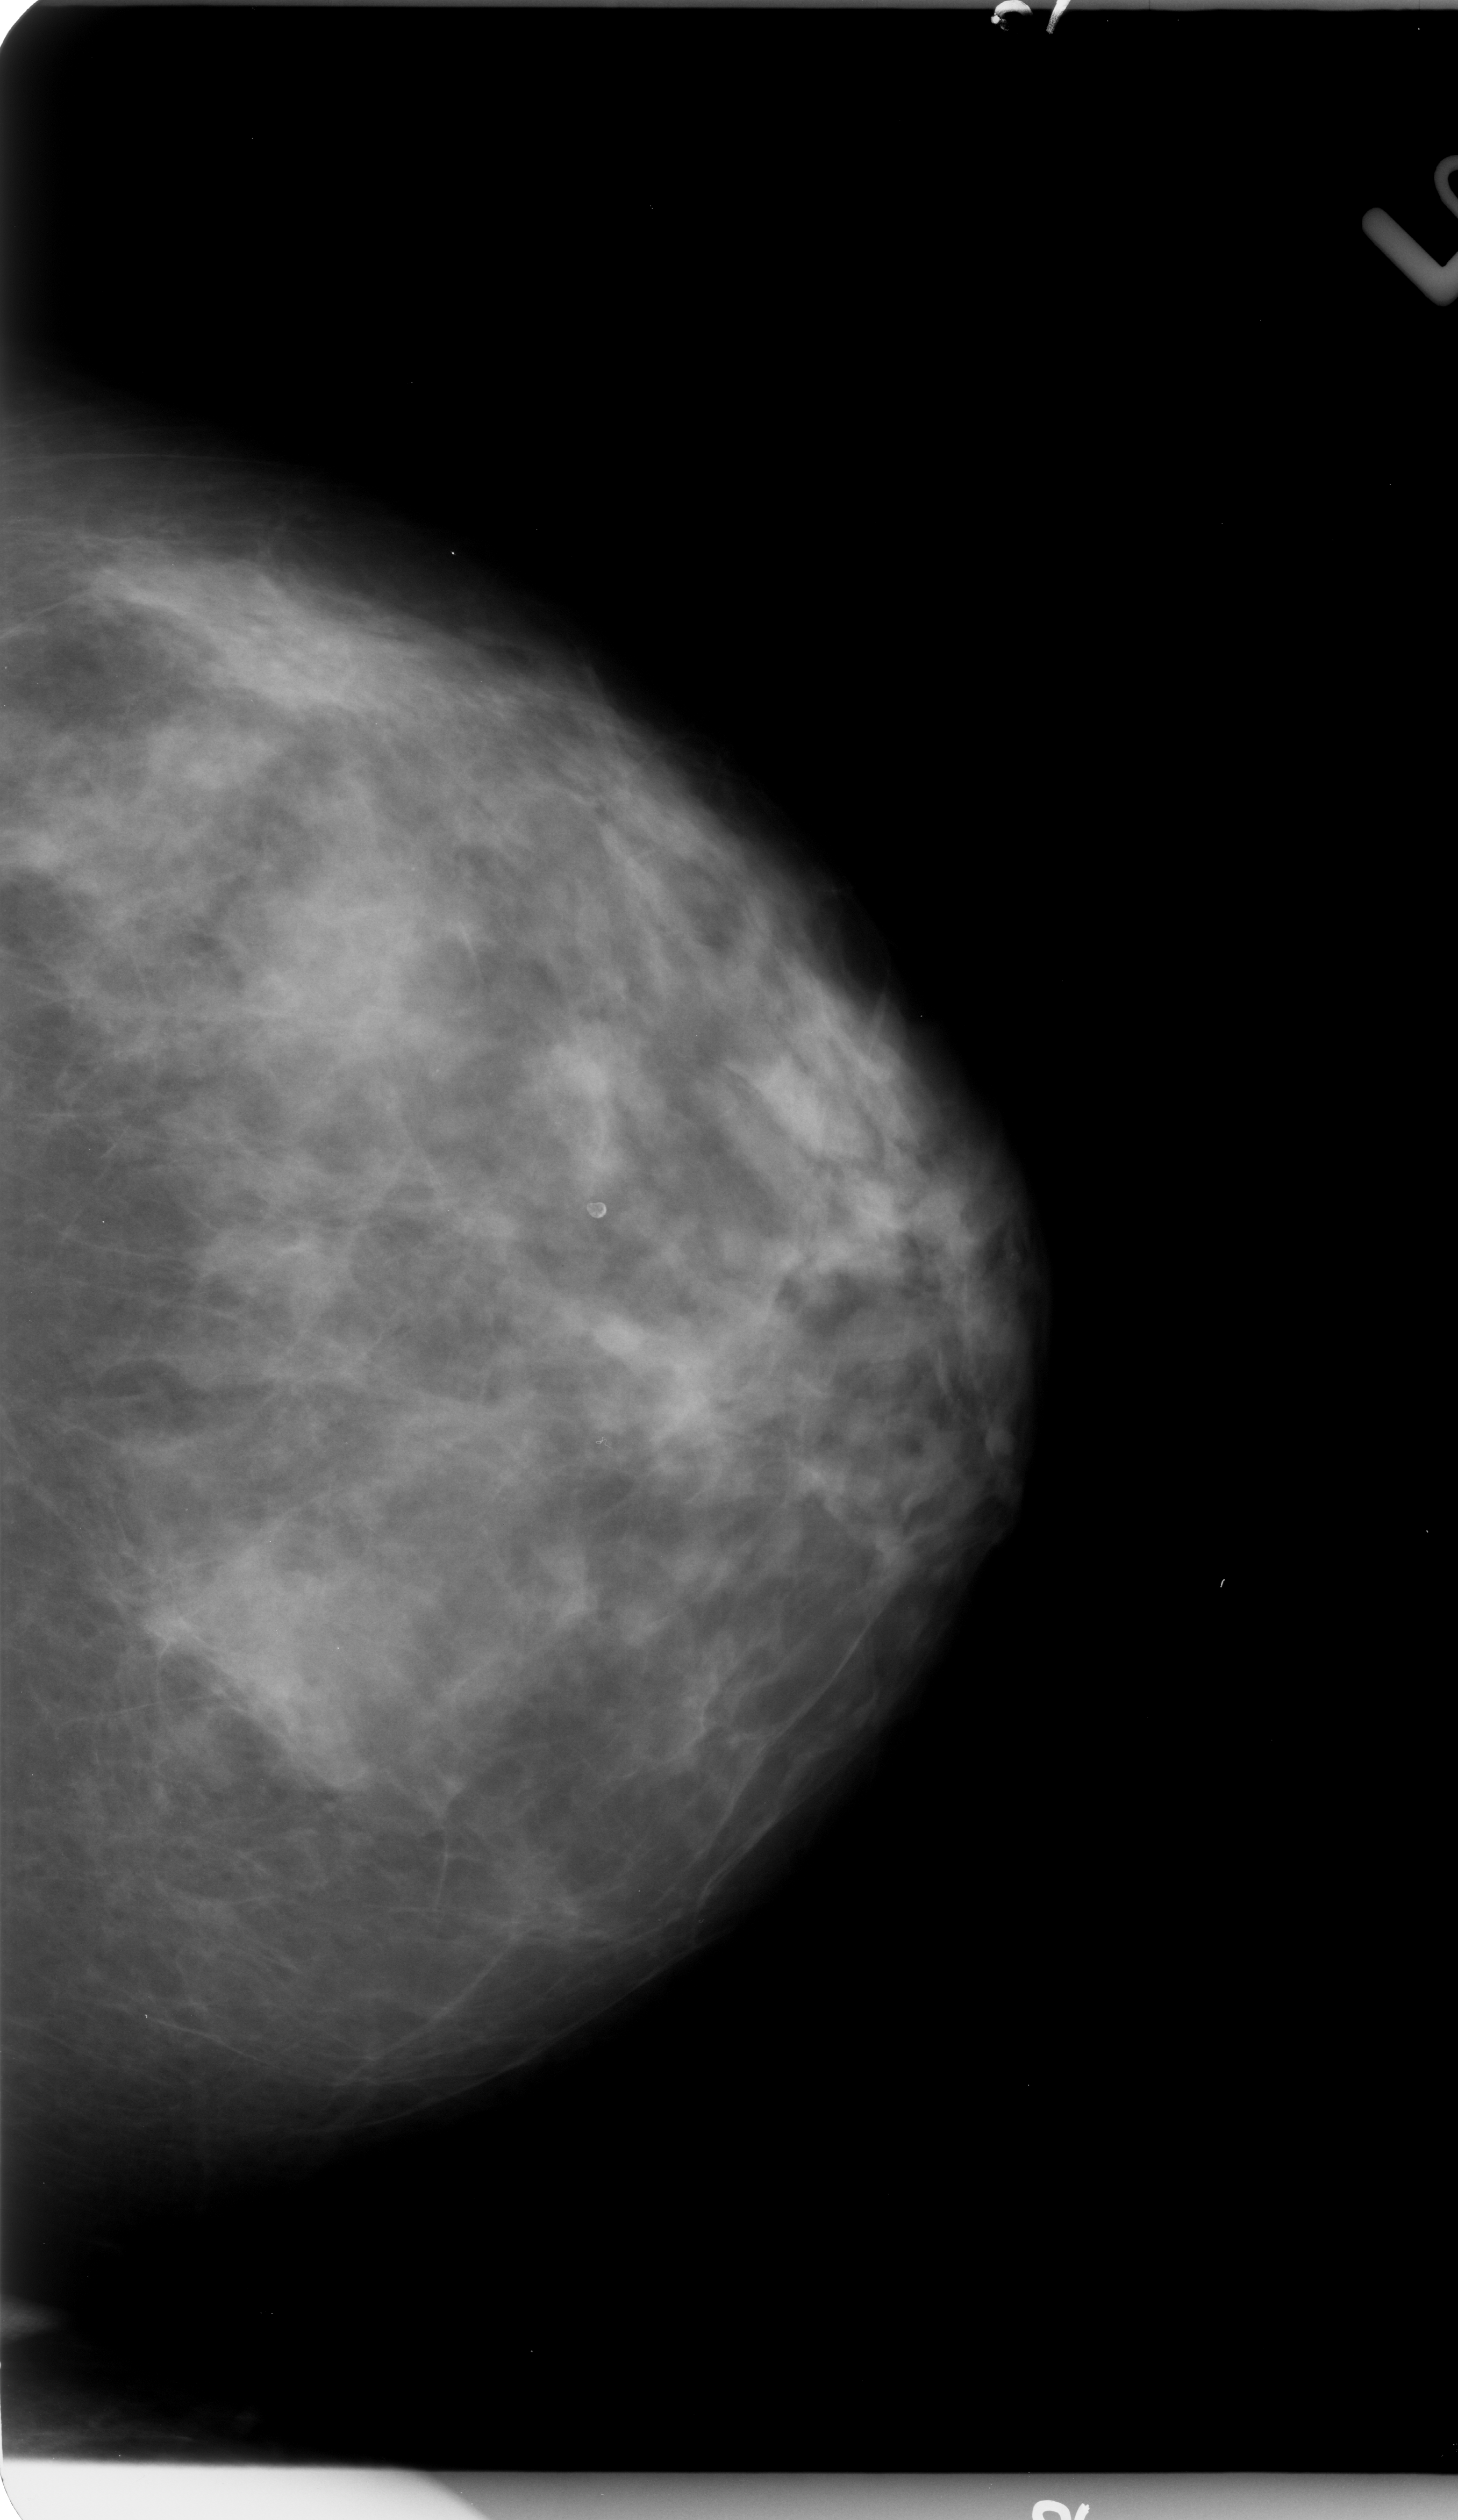
Scanned film-screen mammogram; left breast; CC view; BI-RADS breast density category 3 (scale 1–4).
Marked findings (only marked abnormalities are described; nothing is implied about the rest of the image): calcifications, morphology punctate, distribution clustered; BI-RADS assessment category 3; pathology result (as recorded, not read from the image): benign.